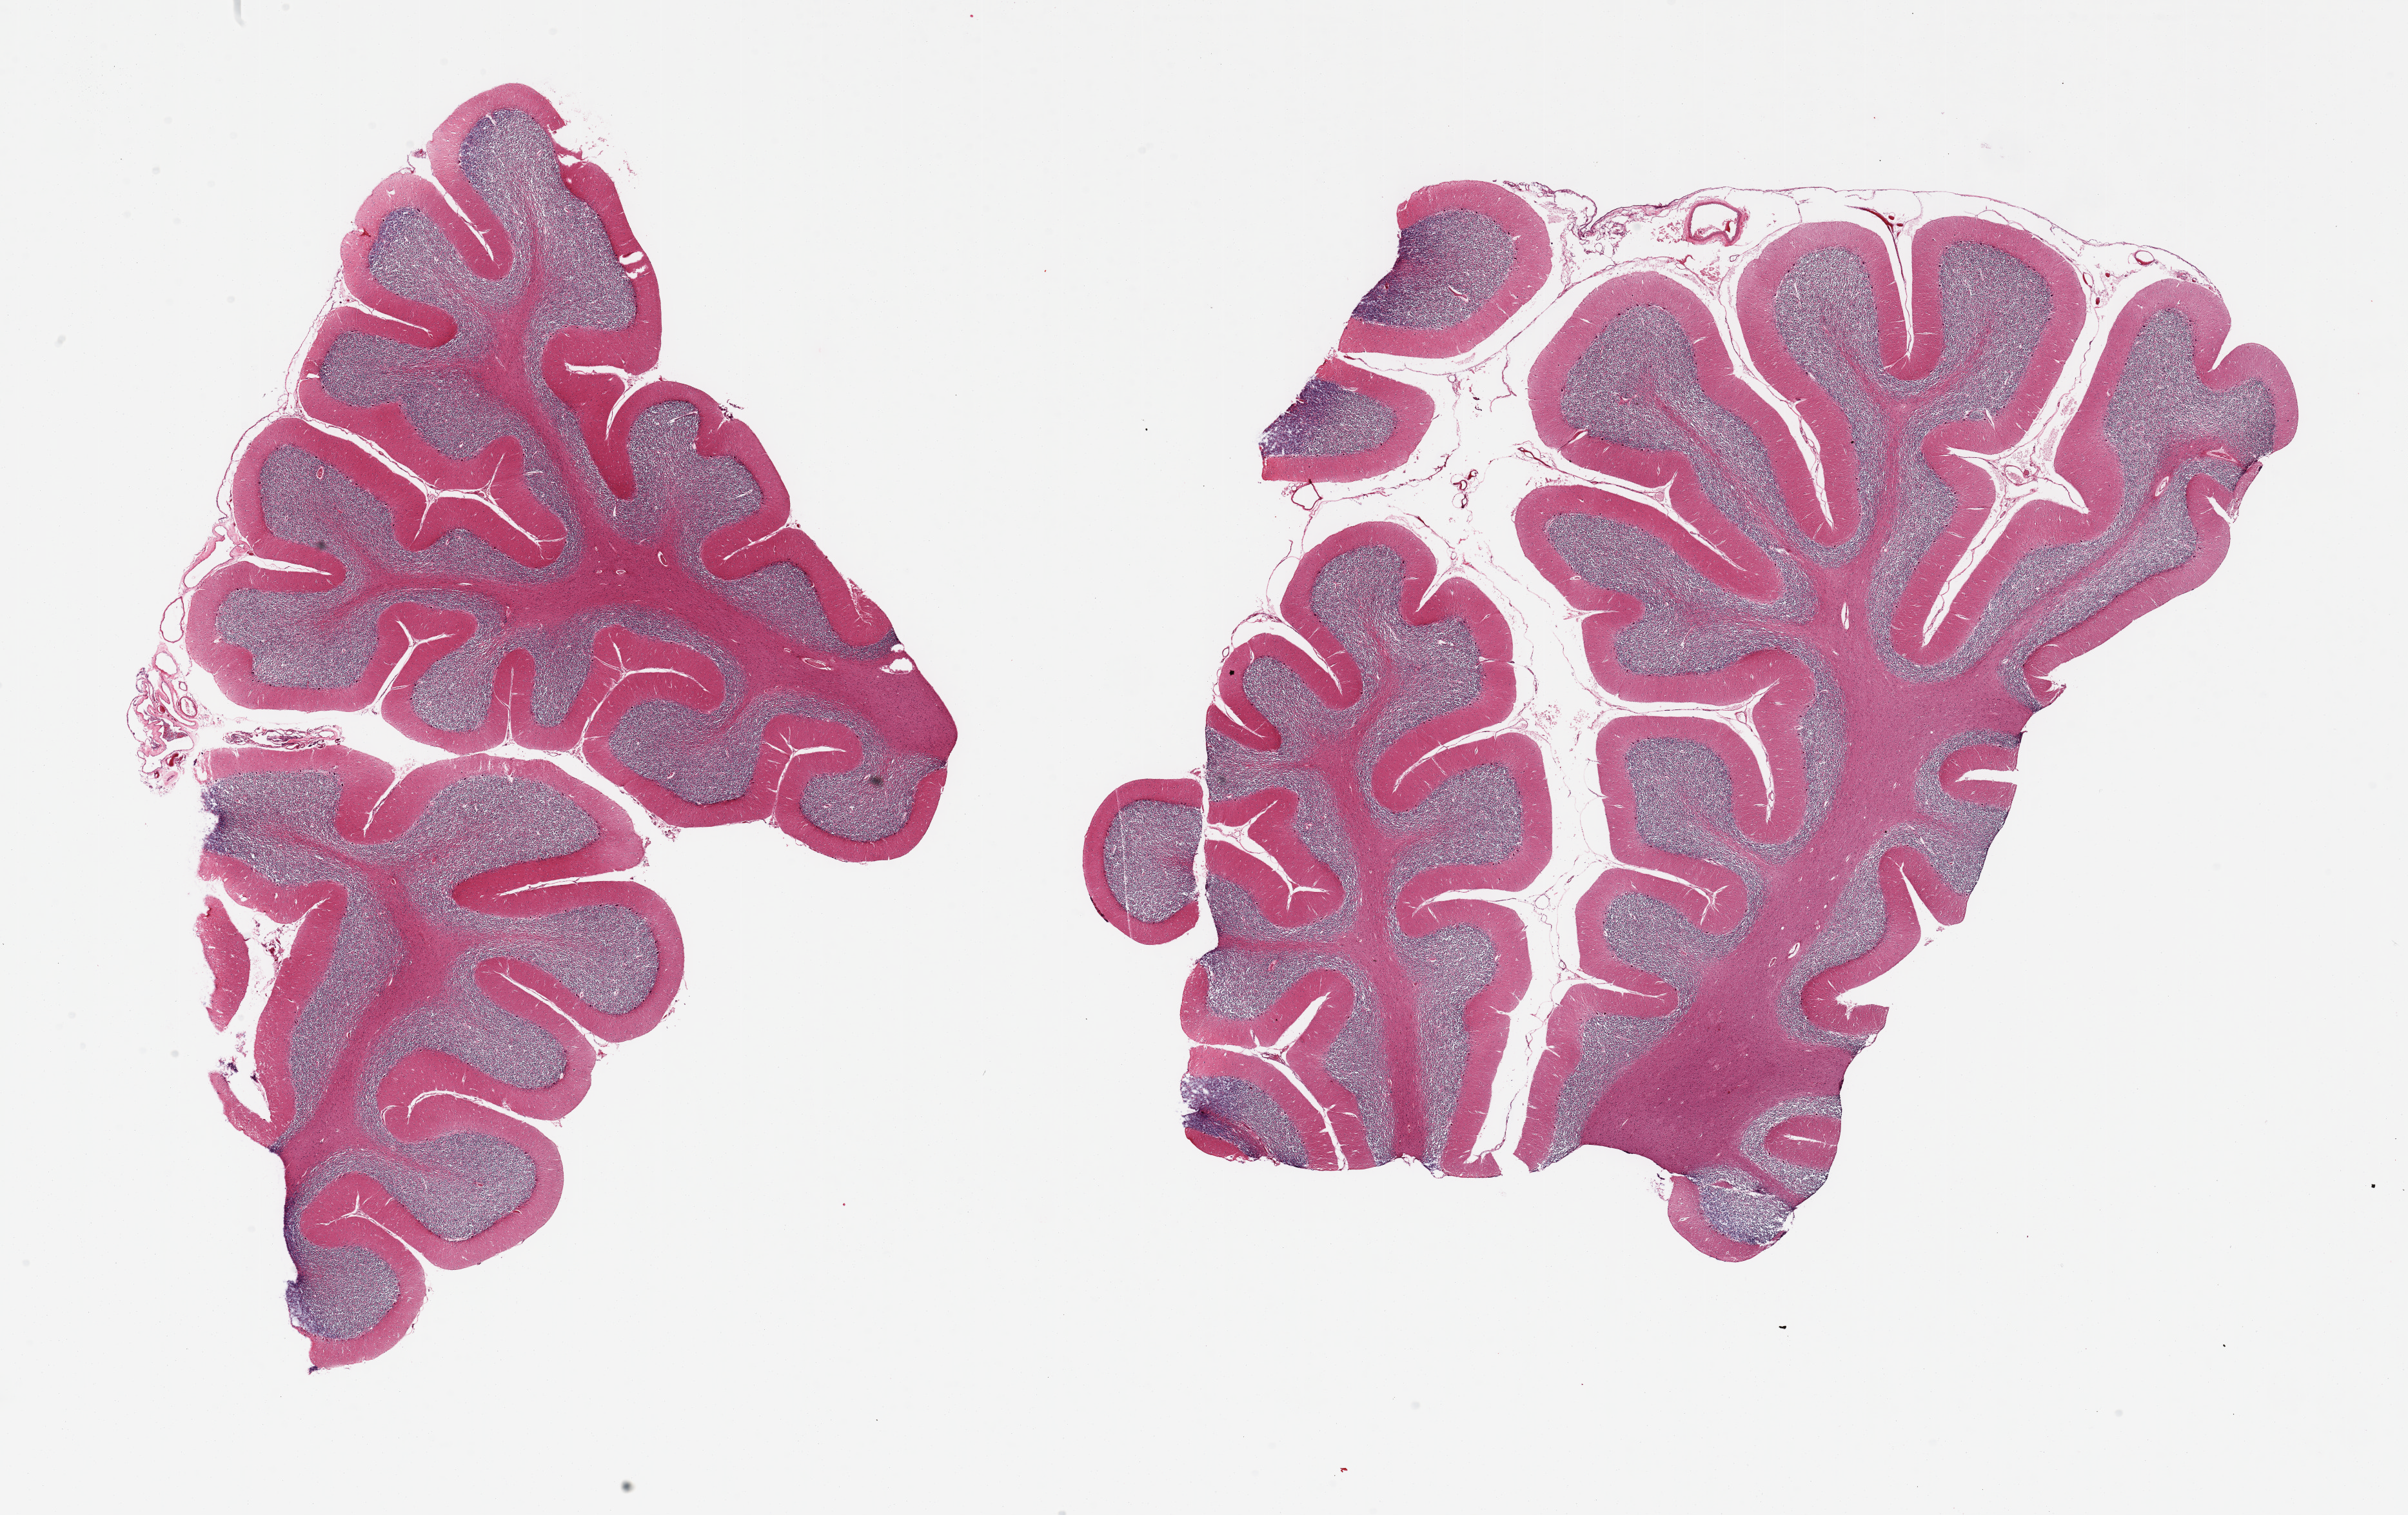
Hematoxylin and eosin (H&E) whole-slide image, whole scanned area (about 29.5 x 18.6 mm) shown as a low-resolution overview, PAXgene-fixed paraffin-embedded (PFPE) section, section of cerebellum (target tissue), tissue donor sample. Donor sex: male.
Review note (as recorded): 2 pieces; covered by meninges; Purkinje cells present.